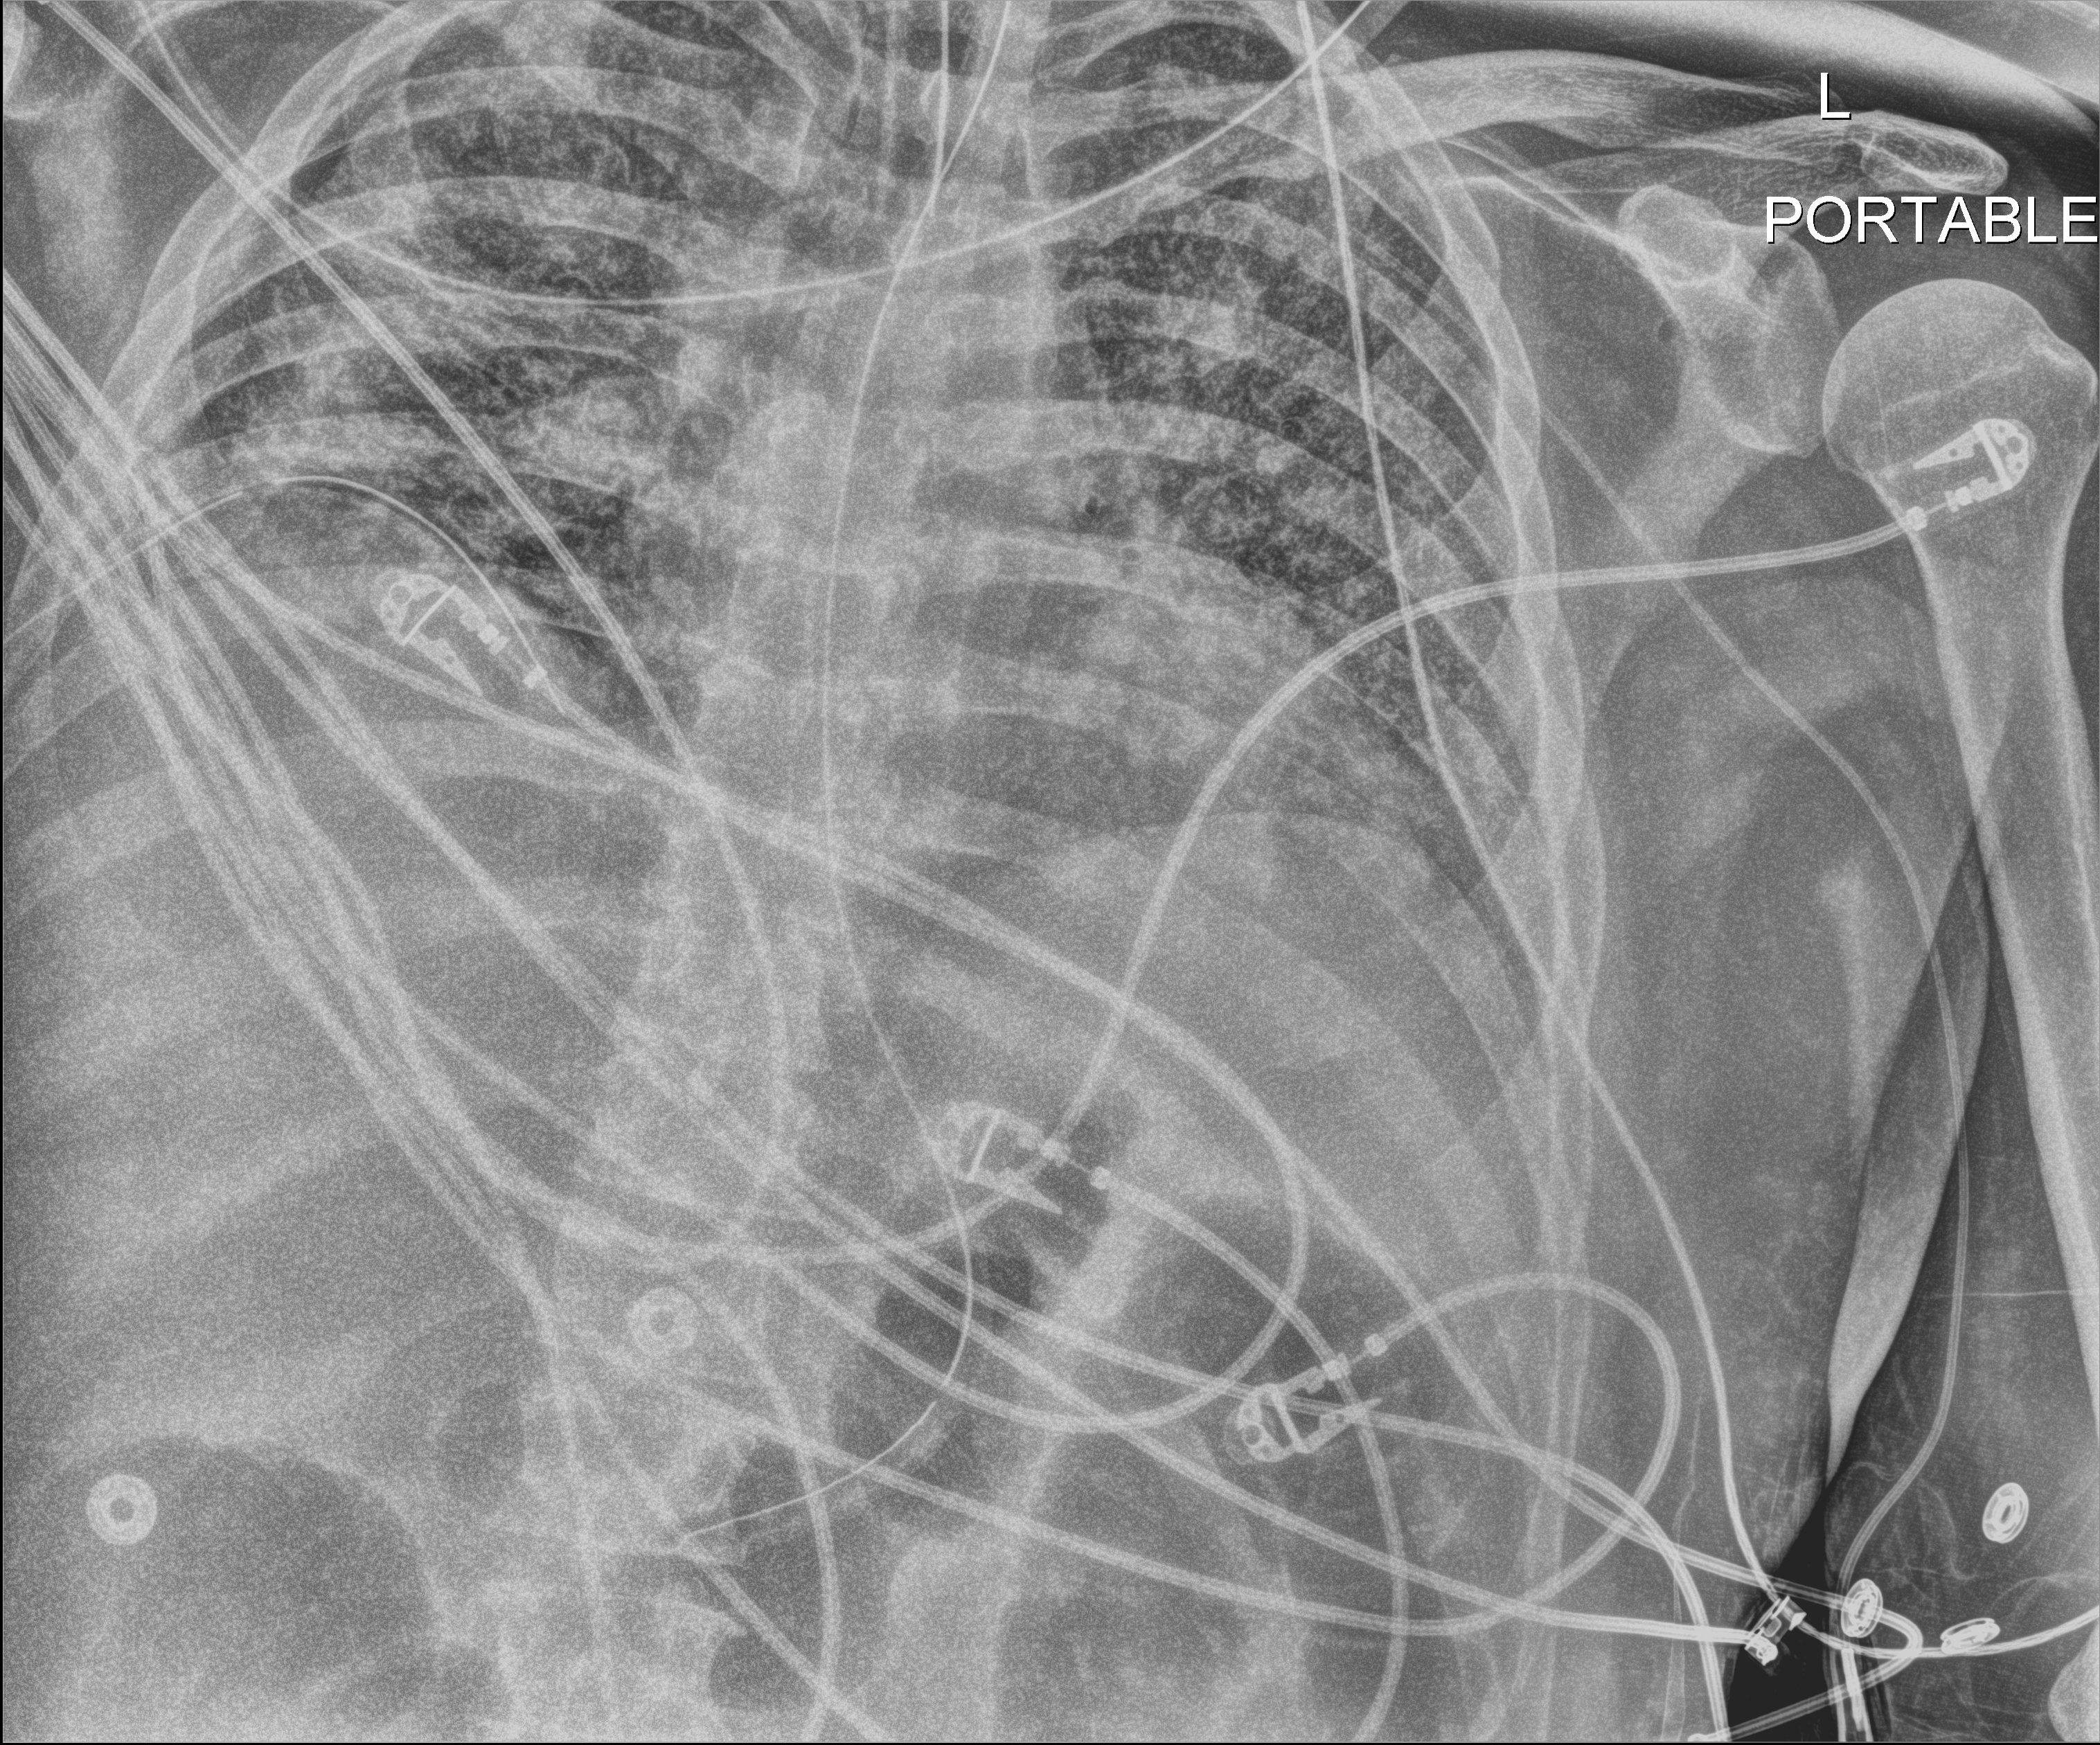
Chest X-ray (portable), anteroposterior (AP) projection. Patient hospitalised with COVID-19; male, aged 18–59 years.
From the hospital-stay record, not from the radiograph (when in the stay this image was taken is not recorded): admitted to intensive care during this hospital stay: yes; diabetes (admission record): no; COPD (admission record): no.